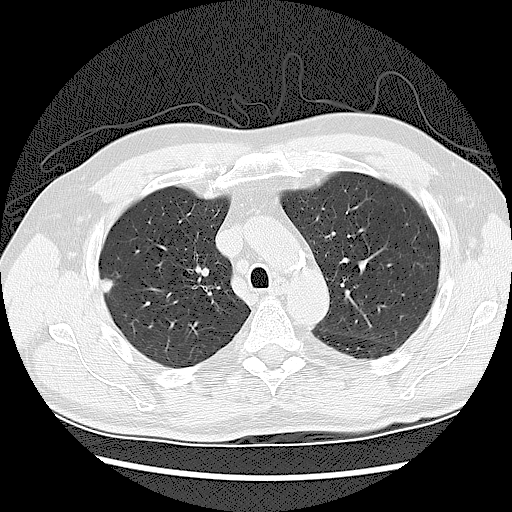
Chest CT (low-dose screening protocol), one axial image; second screening round (one year after baseline); lung window (W 1500 / L -600 HU); 2.5 mm slice thickness. Male, age 62 years at enrolment. Former smoker at enrolment.
• Lesion marked by an expert reader, bounding box <91,272,120,297> (left, top, right, bottom; pixels).
• Reader record for this screening exam (exam-level; its link to the box is not recorded): non-calcified nodule or mass ≥4 mm, right upper lobe, 10 × 10 mm, smooth margins, soft tissue attenuation, pre-existing on the prior screen: yes; interval growth: yes.
• Lung cancer was diagnosed 6 days after this screen: adenocarcinoma, NOS, right upper lobe, poorly differentiated (G3), stage IIB (AJCC 6th edition), 5 mm at pathology.